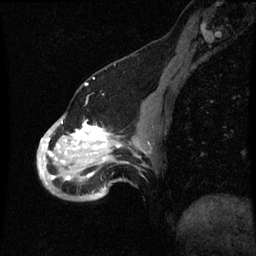
Breast MRI (dynamic contrast-enhanced), one sagittal slice. Position 19 of 60 along the scan axis. Dynamic contrast-enhanced series, image 2 of 3 at this slice position (ordered by acquisition). 1.5 T. TE 4.2 ms, TR 8.9 ms. 2 mm slice thickness. 256 × 256 image matrix, field of view 200 × 200 mm. Female patient, age 49 years. Case-level facts recorded for this patient, not image findings: setting: breast cancer imaged before/during neoadjuvant chemotherapy; receptor status: HR-positive, HER2-negative.
Annotated regions visible in this slice (semi-automatically segmented with operator editing):
- analysis volume of interest (the breast-tissue region the enhancement analysis was run in; not a lesion): bounding box <38,100,151,199> (left, top, right, bottom; pixels)
- tumour enhancement mask (voxels above the 70 % enhancement threshold inside the analysis volume of interest): <40,122,109,181>